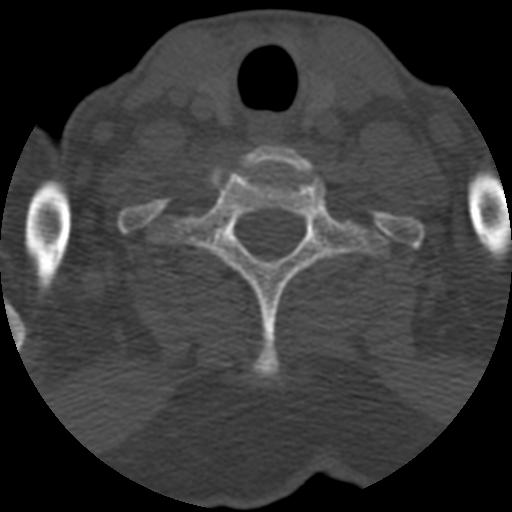
CT including the spine, one axial slice. Slice 520 of 708 in the series (ordered by position). 120 kVp. One of 3 acquisitions stored at this slice position. Bone window (W 1800 / L 400 HU). 1.25 mm slice thickness. 512 × 512 image matrix. Patient age 55 years. From the clinical record (not read from this slice): primary cancer: colon; vertebrae with lytic lesions (as recorded): T12, L1, L5.
Structures marked on this image (semi-automatically segmented with operator editing):
- T1 vertebra: bounding box <150,167,387,380> (left, top, right, bottom; pixels)